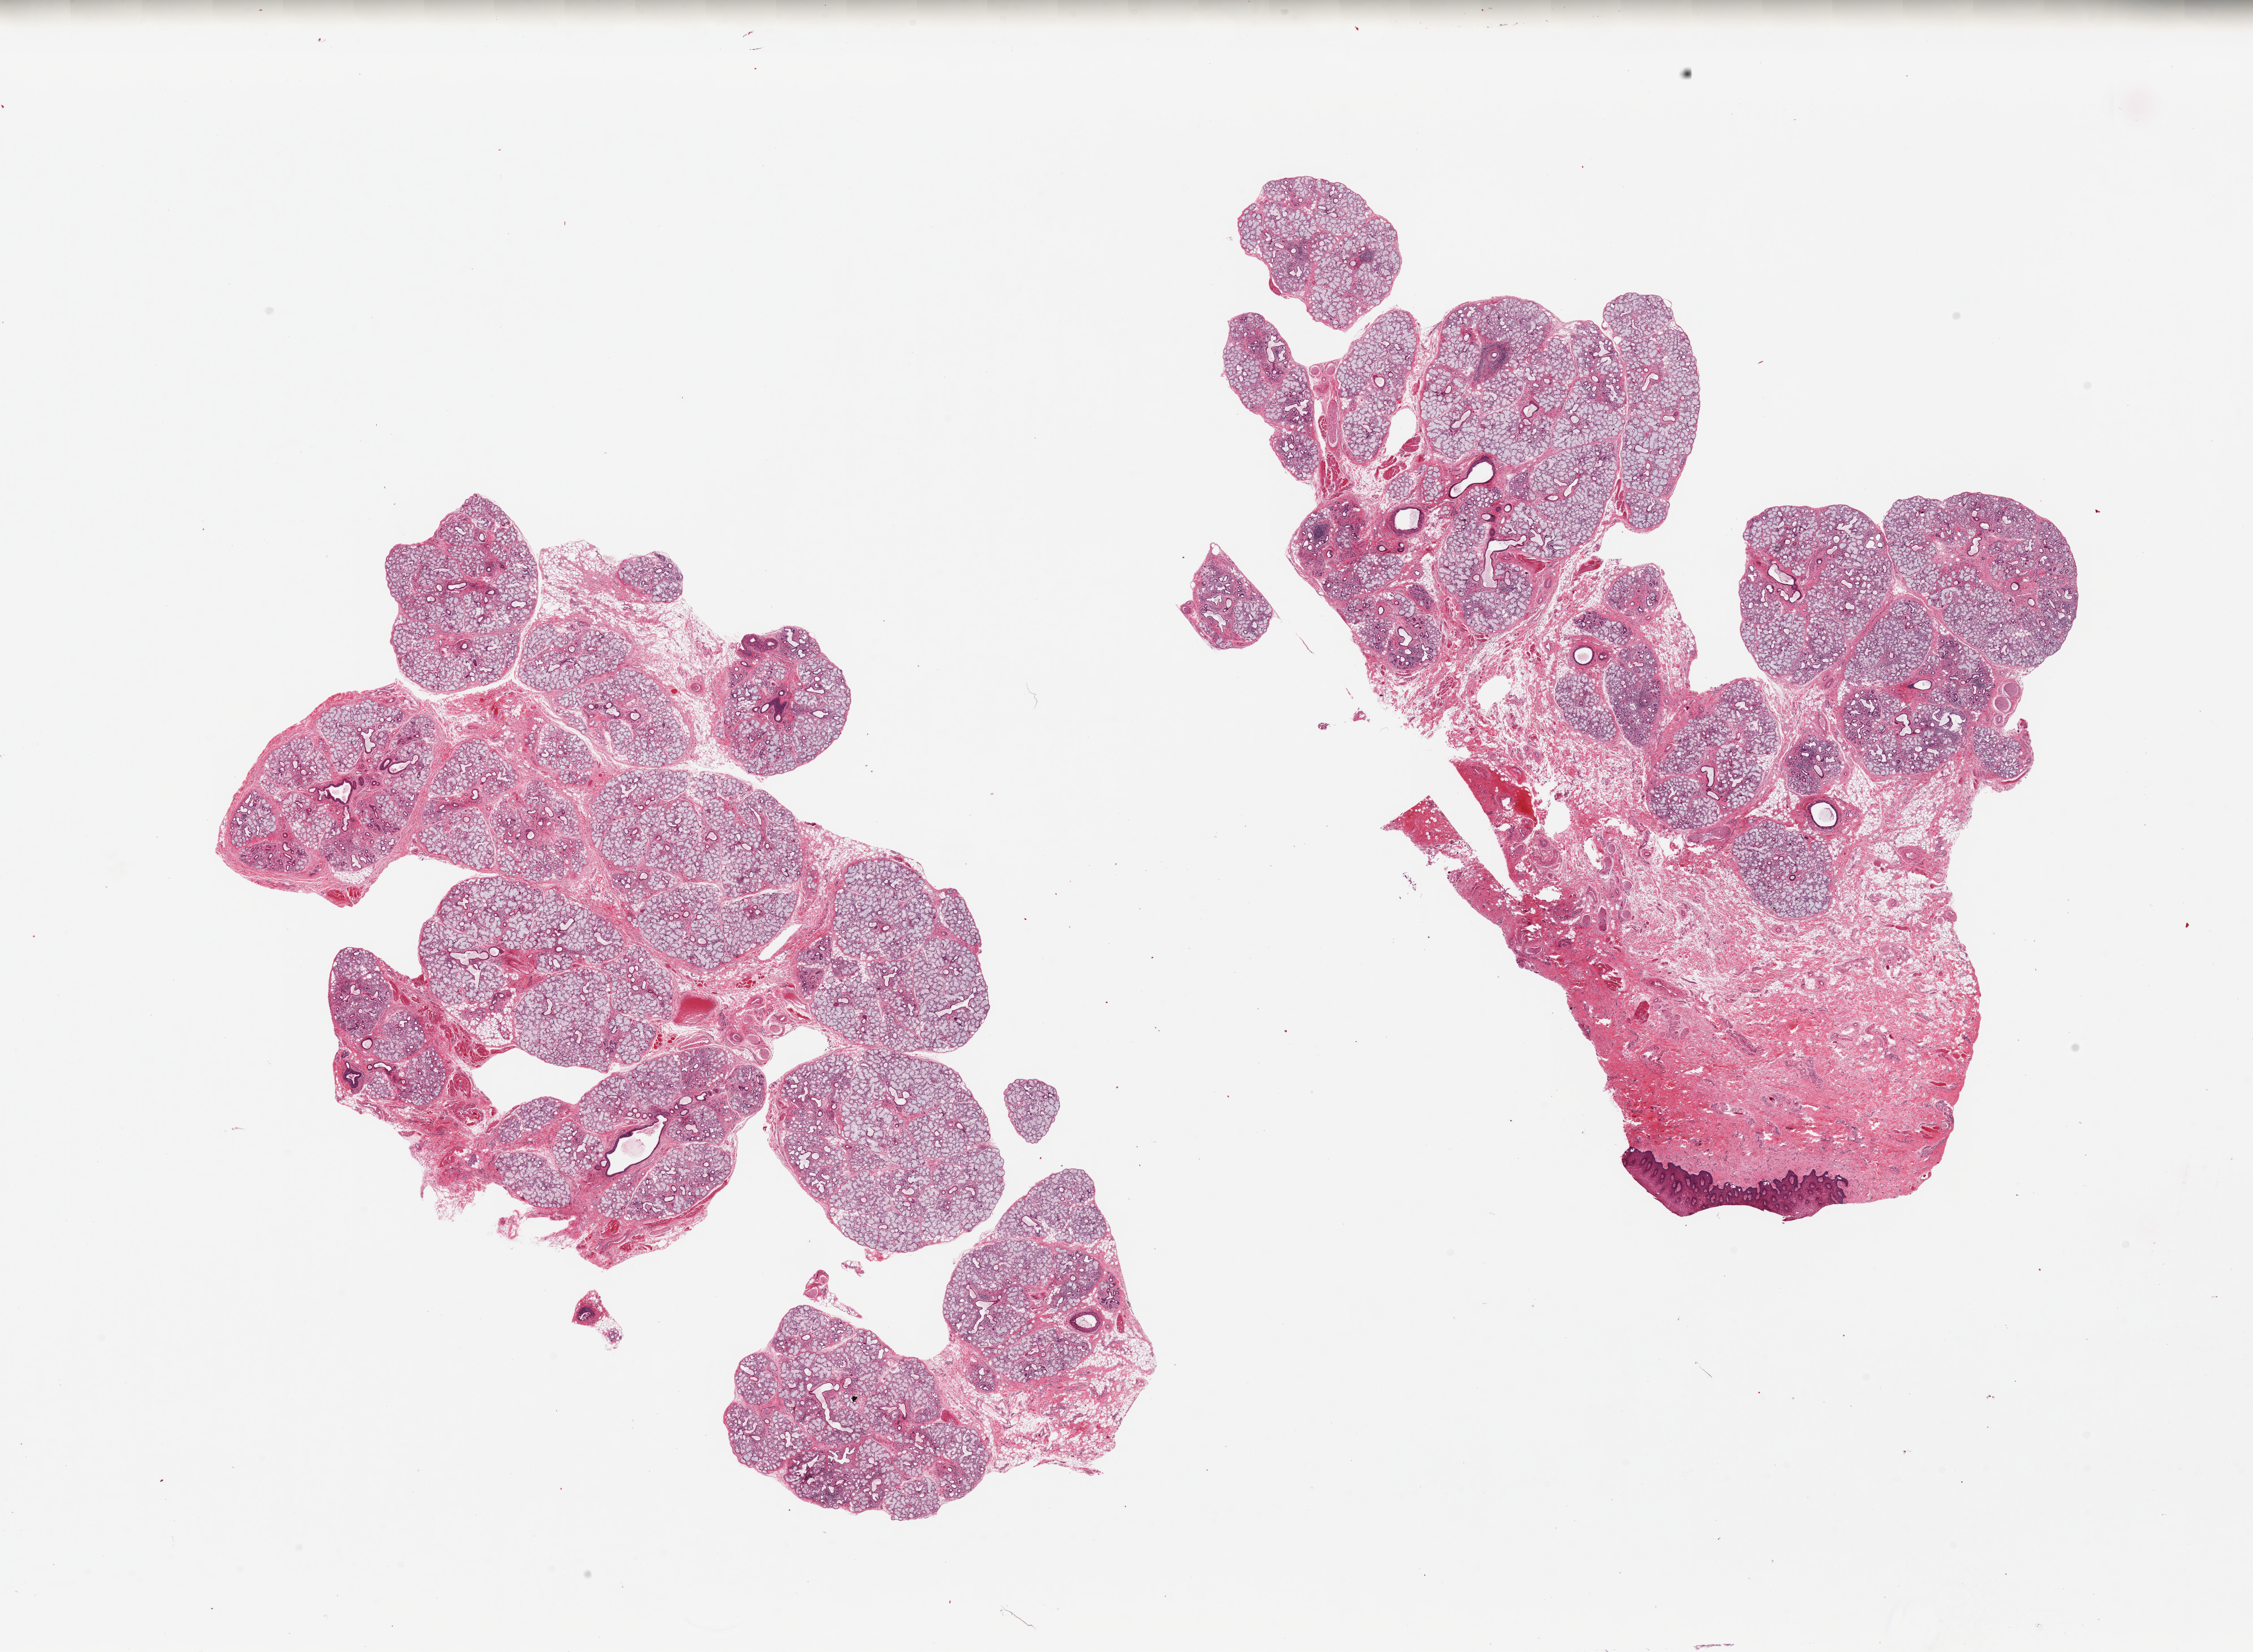
Whole-slide image, haematoxylin and eosin stain, brightfield — a low-resolution overview of the entire scanned area, about 31.5 x 23.1 mm (slide scanned at 20x), PAXgene-fixed, paraffin-embedded tissue, section of minor salivary gland (target tissue), tissue donor sample. Donor sex: male.
Pathologist's review note for this sample: 2 pieces, 1 has good salivary gland with <5% fat & stroma; other is 50% gland [with focal atrophy/chronic inflammation], 50% lip and fibrofatty stroma.